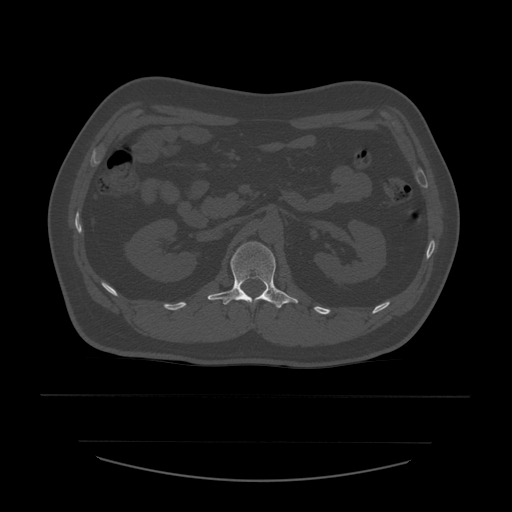
CT including the spine, one axial slice. Bone window (W 1800 / L 400 HU). 1.25 mm slice thickness. 512 × 512 image matrix. Patient age 44 years. Case-level facts recorded for this patient, not image findings: primary cancer: soft tissue sarcoma.
Structures marked on this image (semi-automatic segmentation, software-assisted and operator-edited):
- L1 vertebra: bounding box [x1, y1, x2, y2] px = [208, 242, 299, 309]